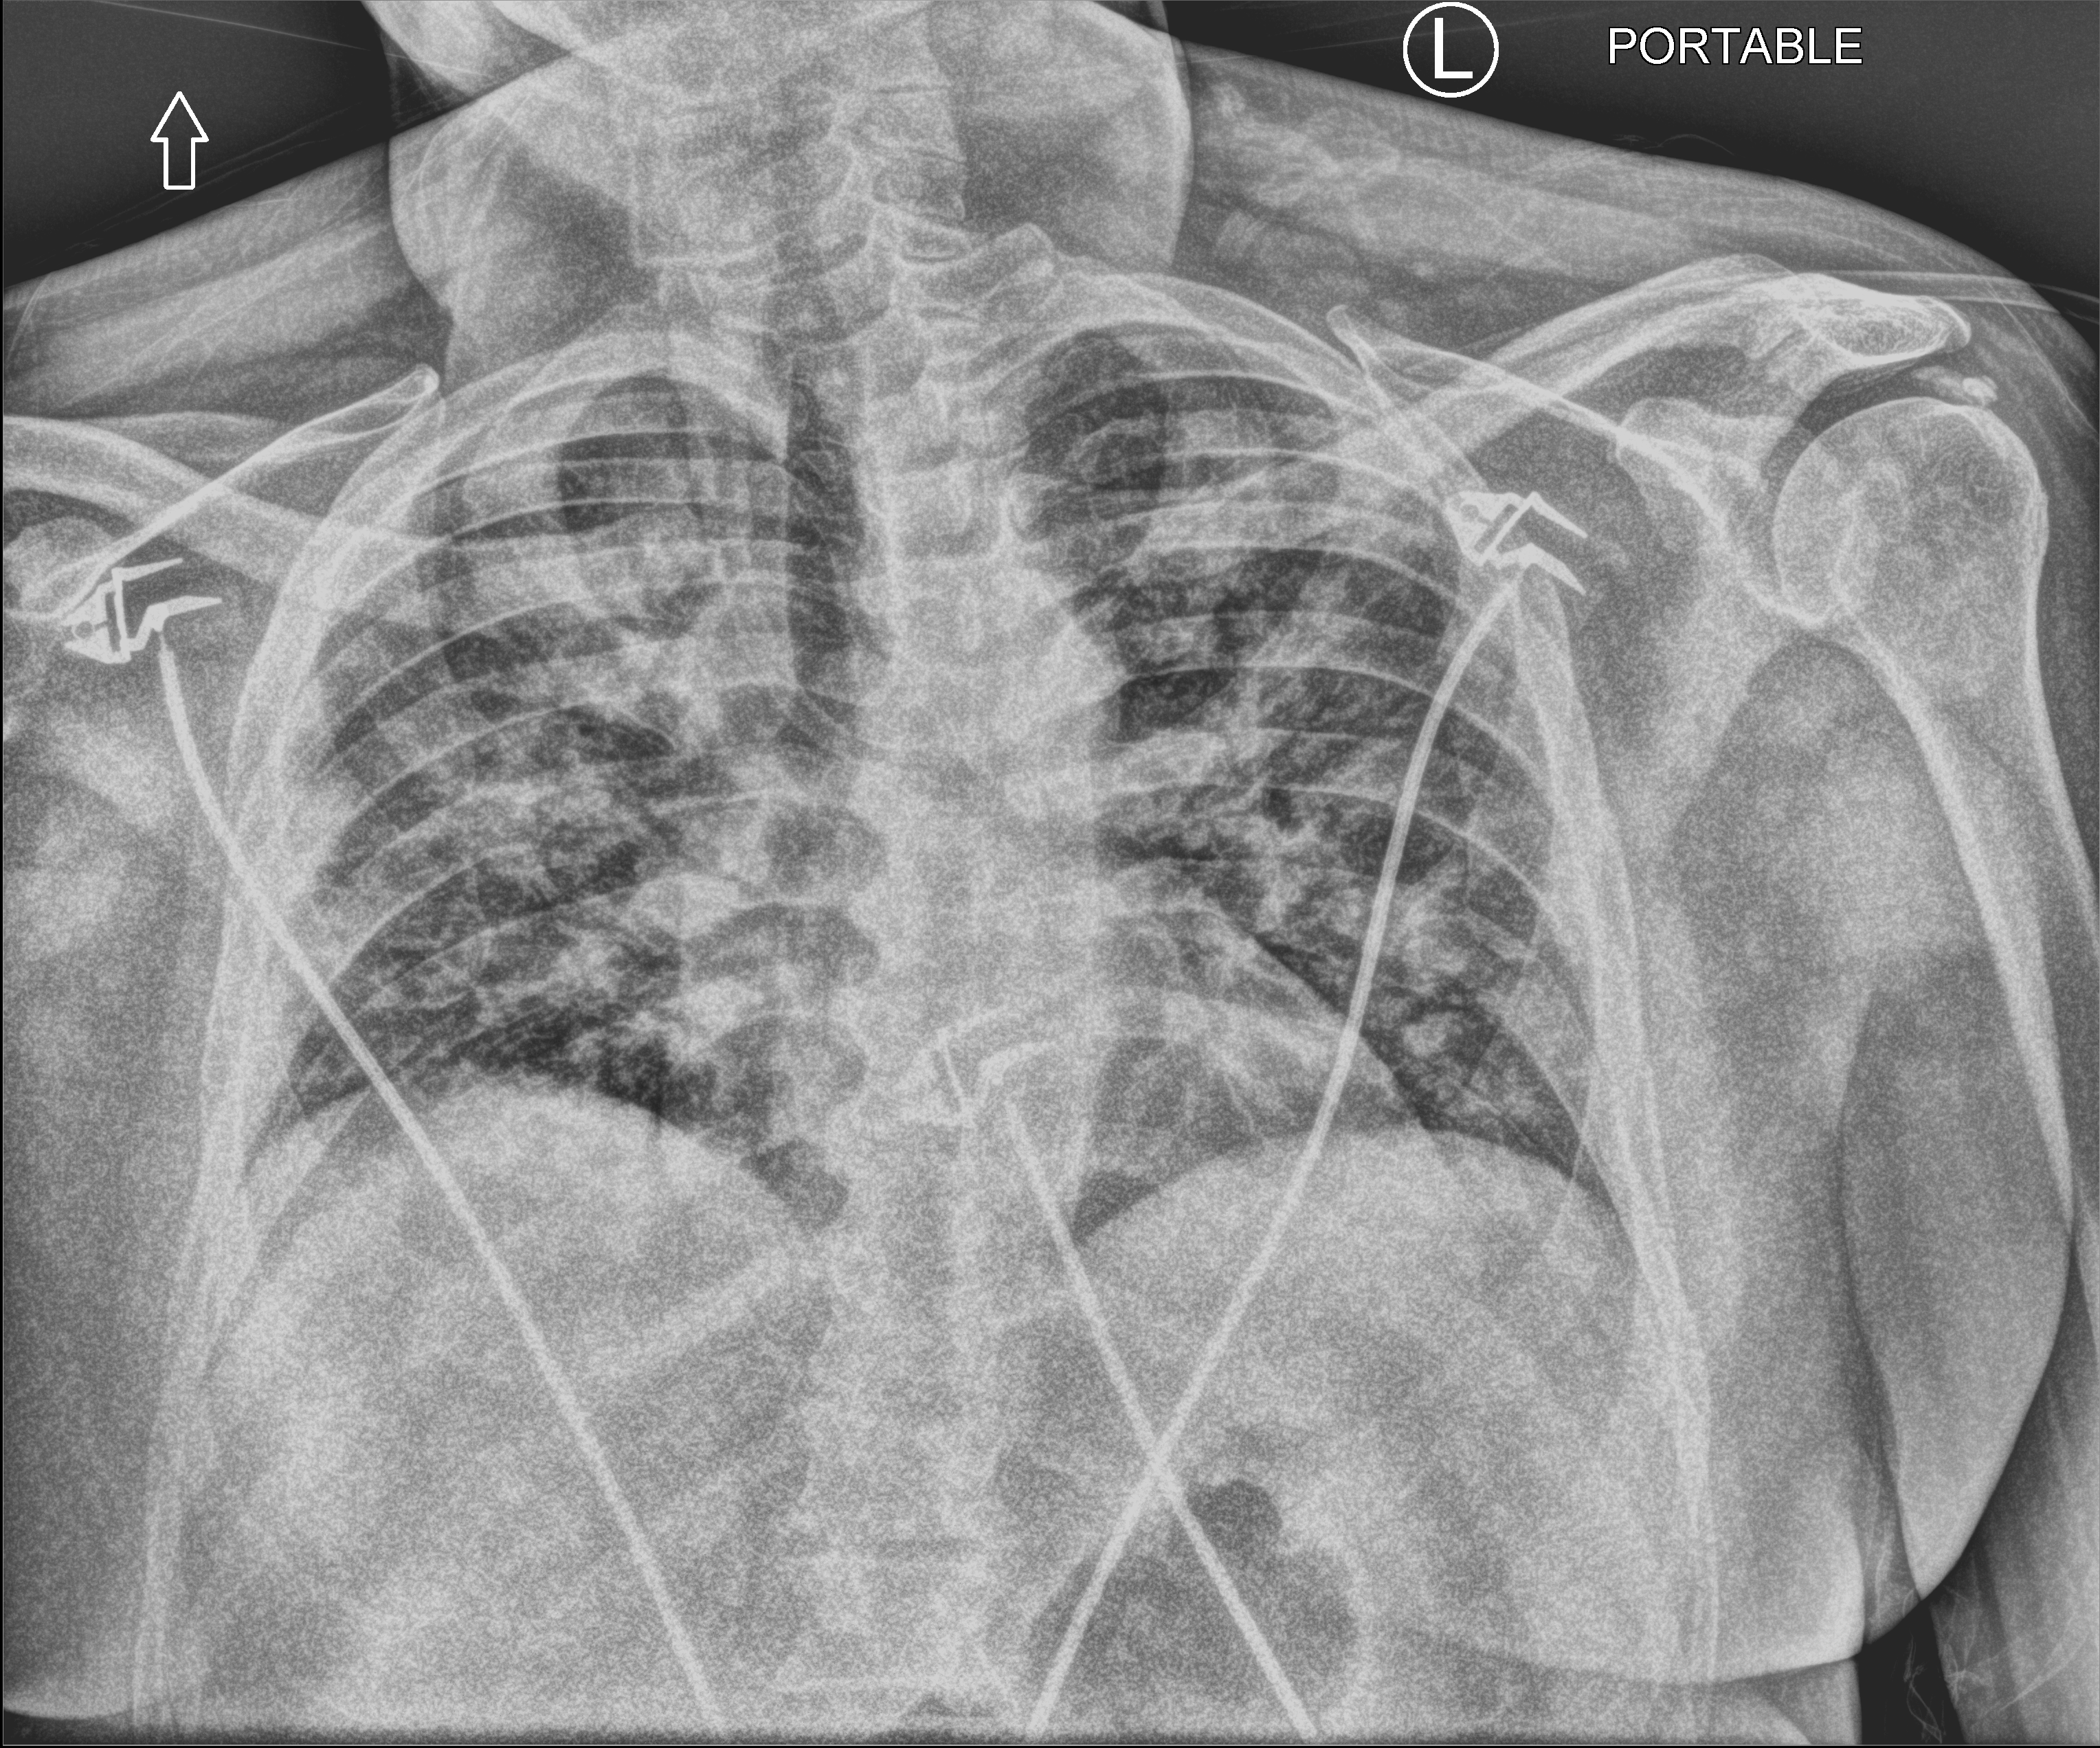
Bedside chest radiograph (computed radiography), anteroposterior (AP) projection. Male patient hospitalised with COVID-19, age 60–74 years.
From the hospital-stay record, not from the radiograph (when in the stay this image was taken is not recorded): diabetes (admission record): yes; mechanically ventilated during this hospital stay: no; admitted to intensive care during this hospital stay: no.